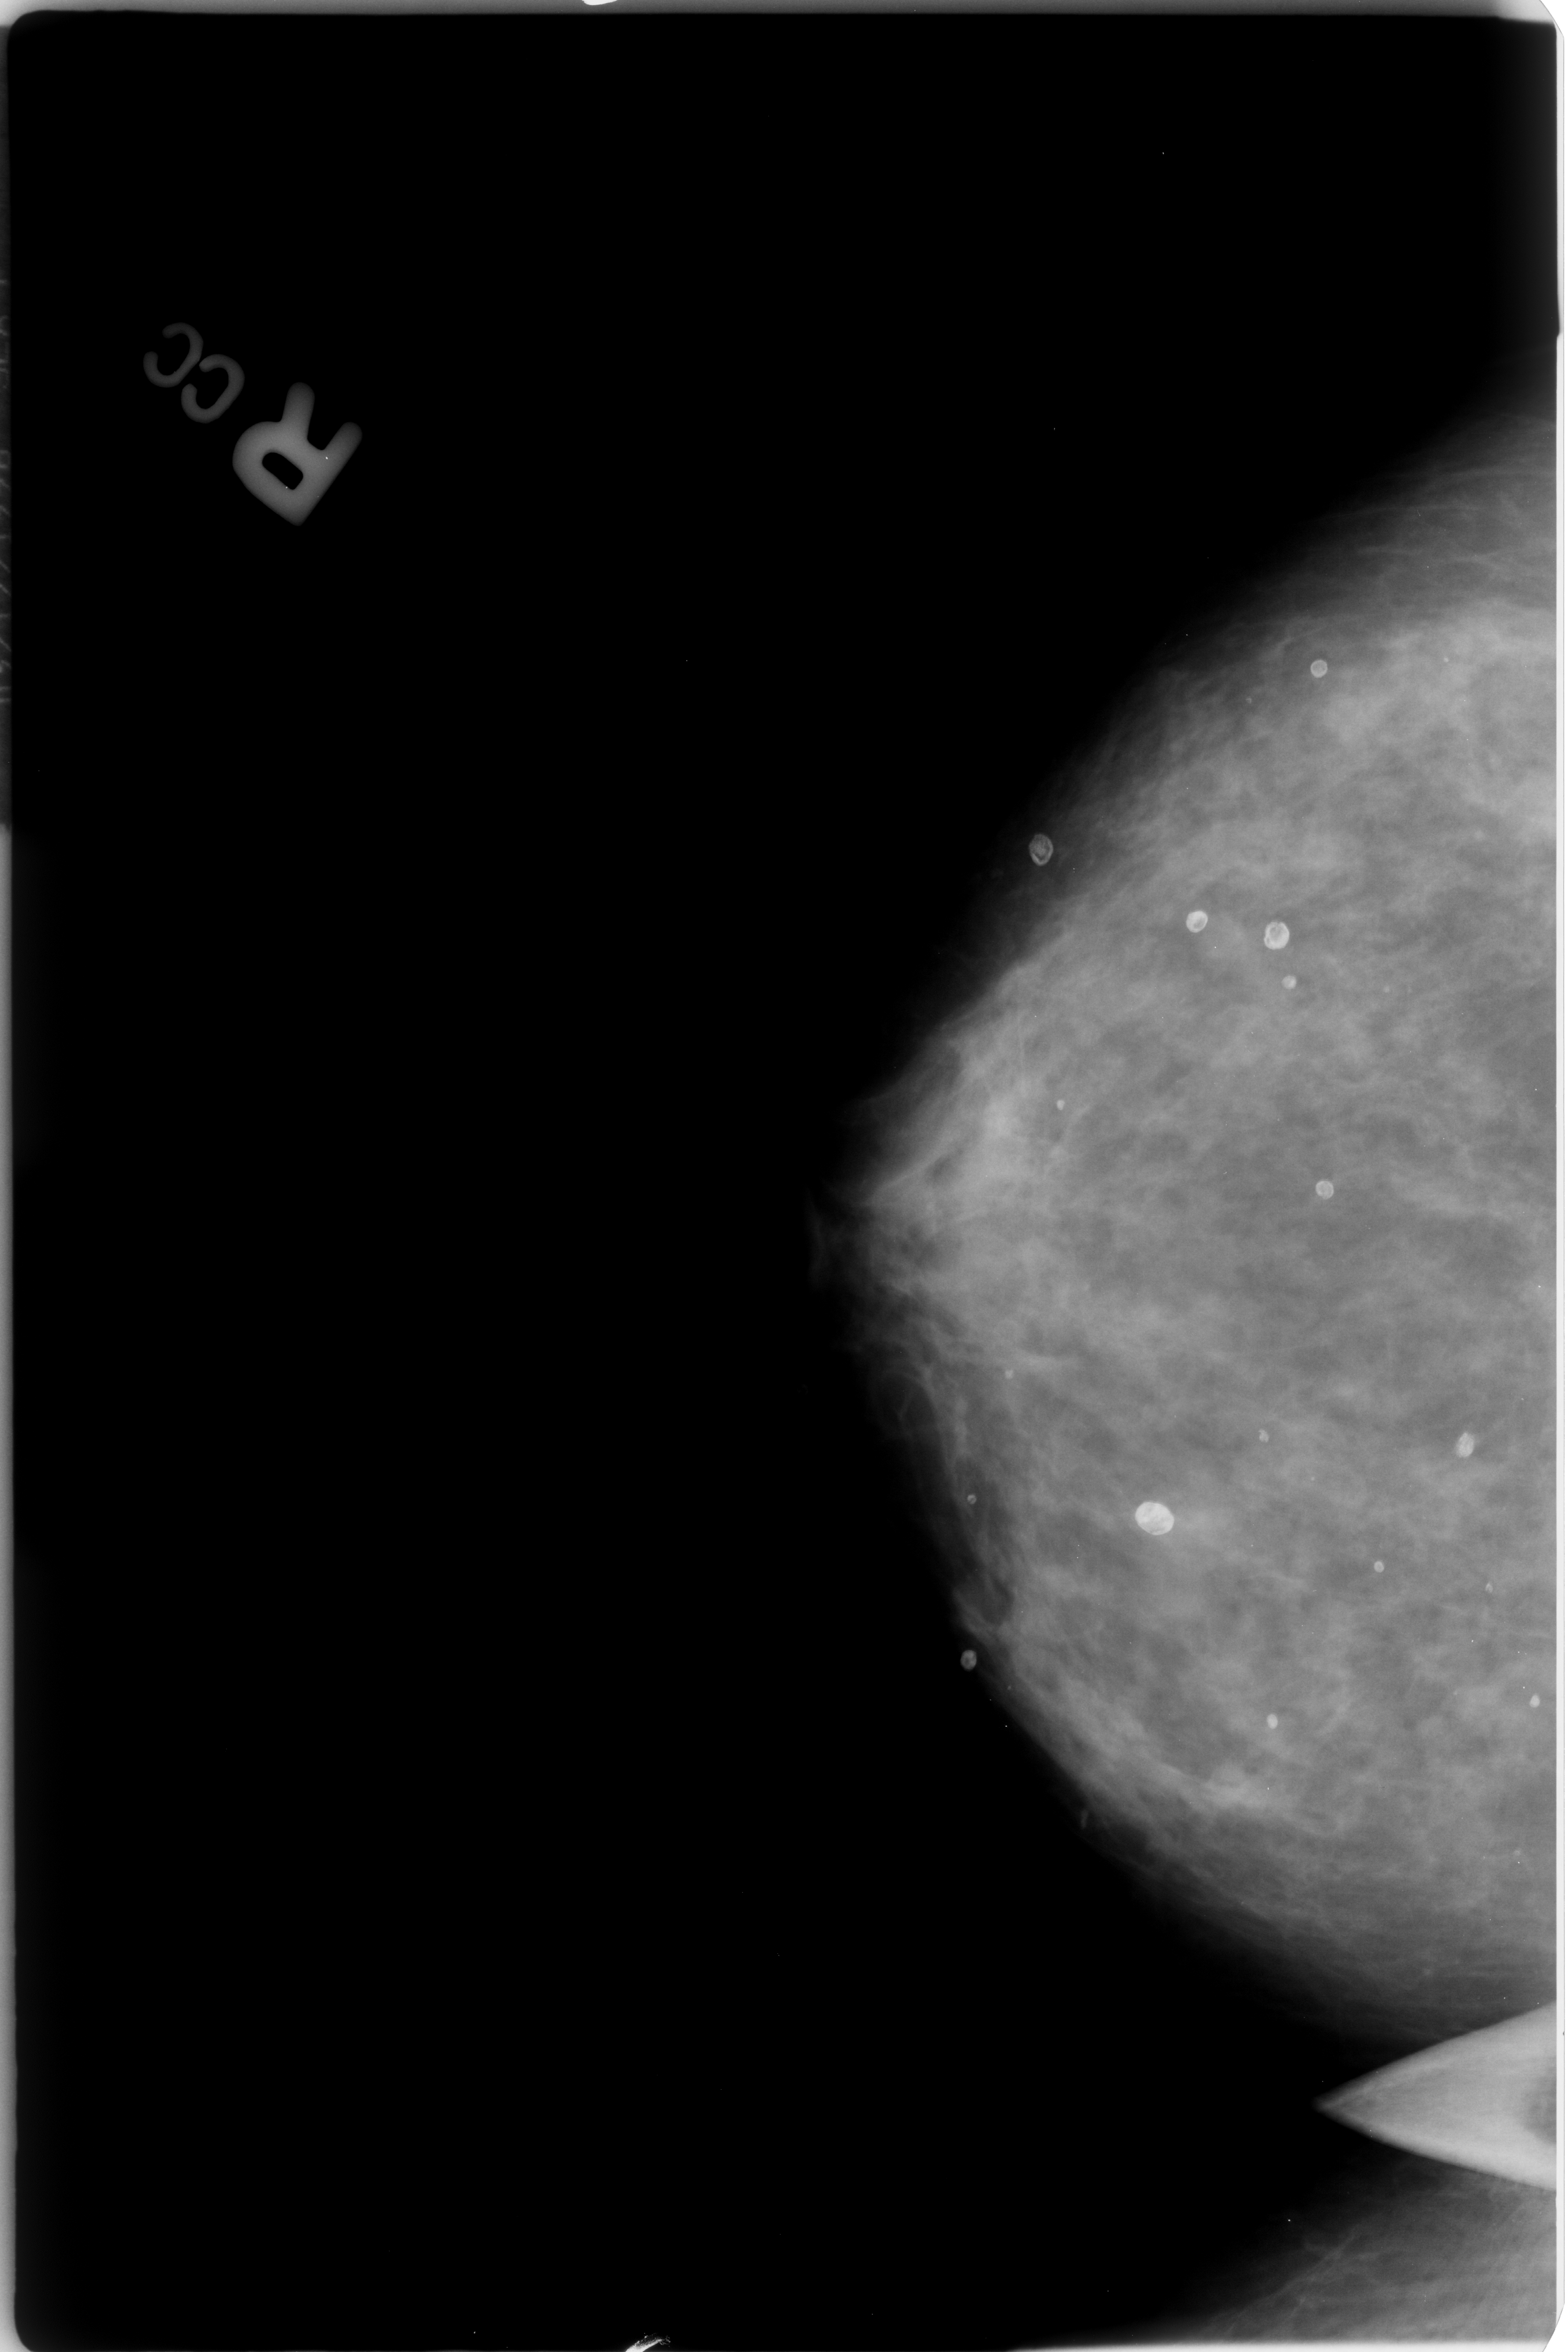
Digitized screen-film mammogram, right breast, CC view, BI-RADS breast density category 3 (scale 1–4).
Abnormality record for this image: Finding 1 of 6: calcifications, morphology round and regular / eggshell; BI-RADS assessment category 2; subtlety rating 3 on a 1 (subtle) to 5 (obvious) scale; benign without callback (not worked up further). Finding 2 of 6: calcifications, morphology round and regular / eggshell; BI-RADS assessment category 2; subtlety rating 3 on a 1 (subtle) to 5 (obvious) scale; benign without callback (not worked up further). Finding 3 of 6: calcifications, morphology round and regular / eggshell; BI-RADS assessment category 2; subtlety rating 3 on a 1 (subtle) to 5 (obvious) scale; benign; no additional work-up was recommended (benign without callback). Finding 4 of 6: calcifications, morphology round and regular / eggshell; BI-RADS assessment category 2; subtlety rating 3 on a 1 (subtle) to 5 (obvious) scale; benign; no additional work-up was recommended (benign without callback). Finding 5 of 6: calcifications, morphology round and regular / eggshell; BI-RADS assessment category 2; benign; no additional work-up was recommended (benign without callback). Finding 6 of 6: calcifications, morphology round and regular / eggshell; BI-RADS assessment category 2; benign without callback (not worked up further).